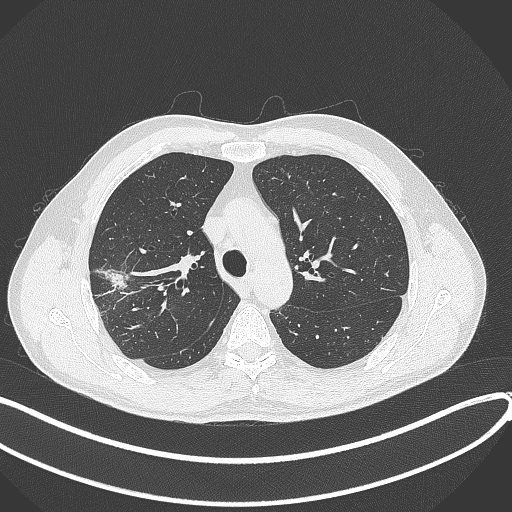
Chest CT, one axial slice; position 300 of 381 along the scan axis; reconstruction kernel B70f; lung window (W 1500 / L -600 HU); 1 mm slice thickness; 512 × 512 image matrix, field of view 400 × 400 mm. Male patient, age 62 years. Case-level facts recorded for this patient, not image findings: clinical TNM (as recorded): T1c N0 M0; histopathological grade: G2-3.
Structures marked on this image (rectangle marked by the reading radiologist):
- lung tumour (recorded histology: adenocarcinoma): bounding box (x1, y1, x2, y2) in pixels: (99, 266, 130, 292)